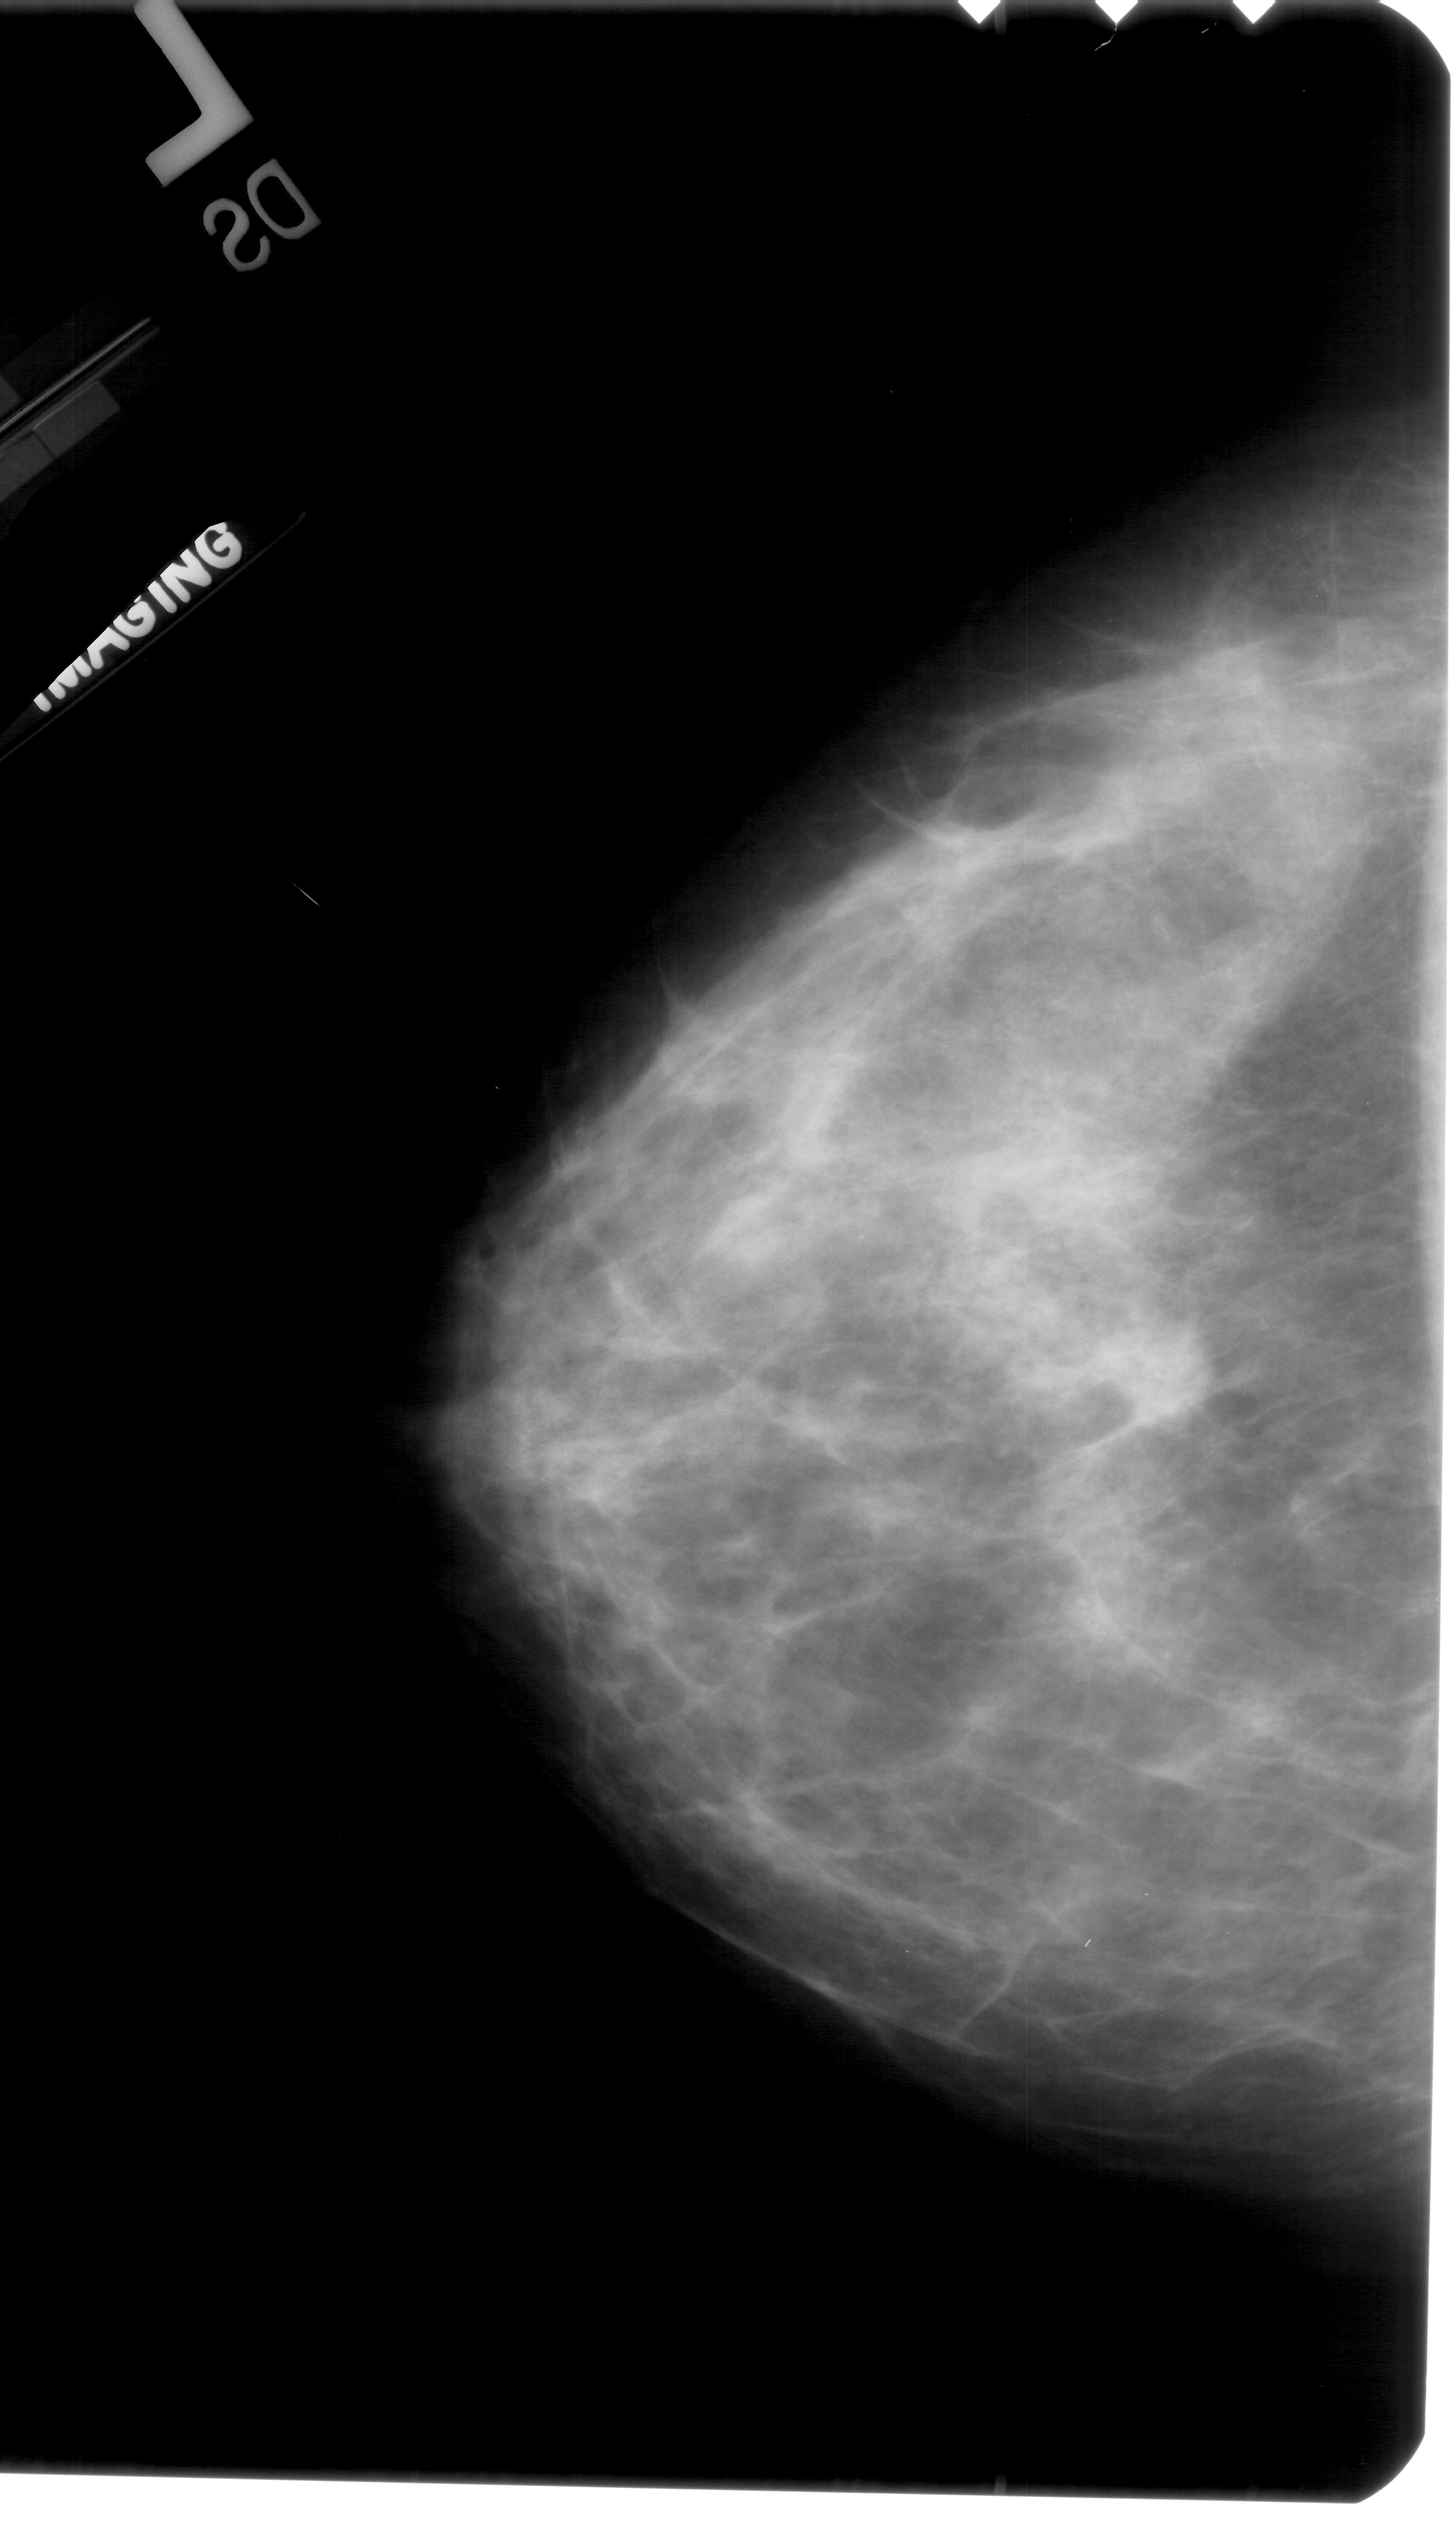
Digitized screen-film mammogram; left breast; CC view; breast composition: extremely dense (BI-RADS density category 4 of 4); 1456 × 2526 image matrix.
Marked abnormalities (boxes around the expert regions of interest):
- mass, shape focal asymmetric density, margins ill defined; BI-RADS assessment category 4; subtlety rating 3 on a 1 (subtle) to 5 (obvious) scale; pathology (as recorded): malignant: bounding box (x1, y1, x2, y2) in pixels: (1091, 1309, 1244, 1446)